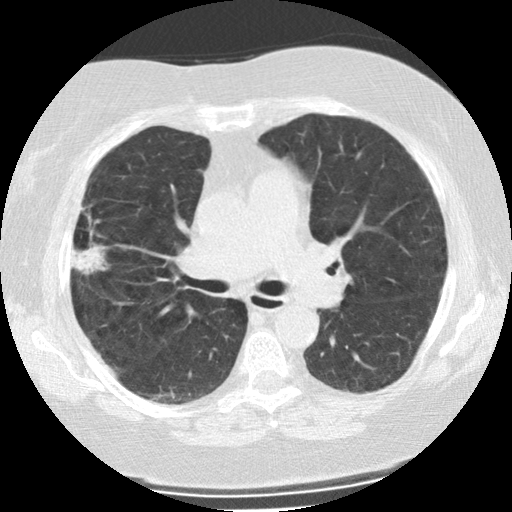
Chest CT (low-dose screening protocol), one axial image, second screening round (one year after baseline), lung window (W 1500 / L -600 HU), 2.5 mm slice thickness, standard (soft-tissue) reconstruction kernel (STANDARD). Female participant, aged 73 years at enrolment. Former smoker at enrolment.
Lesion marked by an expert reader, box from (x=55, y=209) to (x=108, y=282) px. The screening reader recorded 2 non-calcified nodules or masses ≥4 mm on this exam (right upper lobe, left upper lobe); which of them this box marks is not recorded.